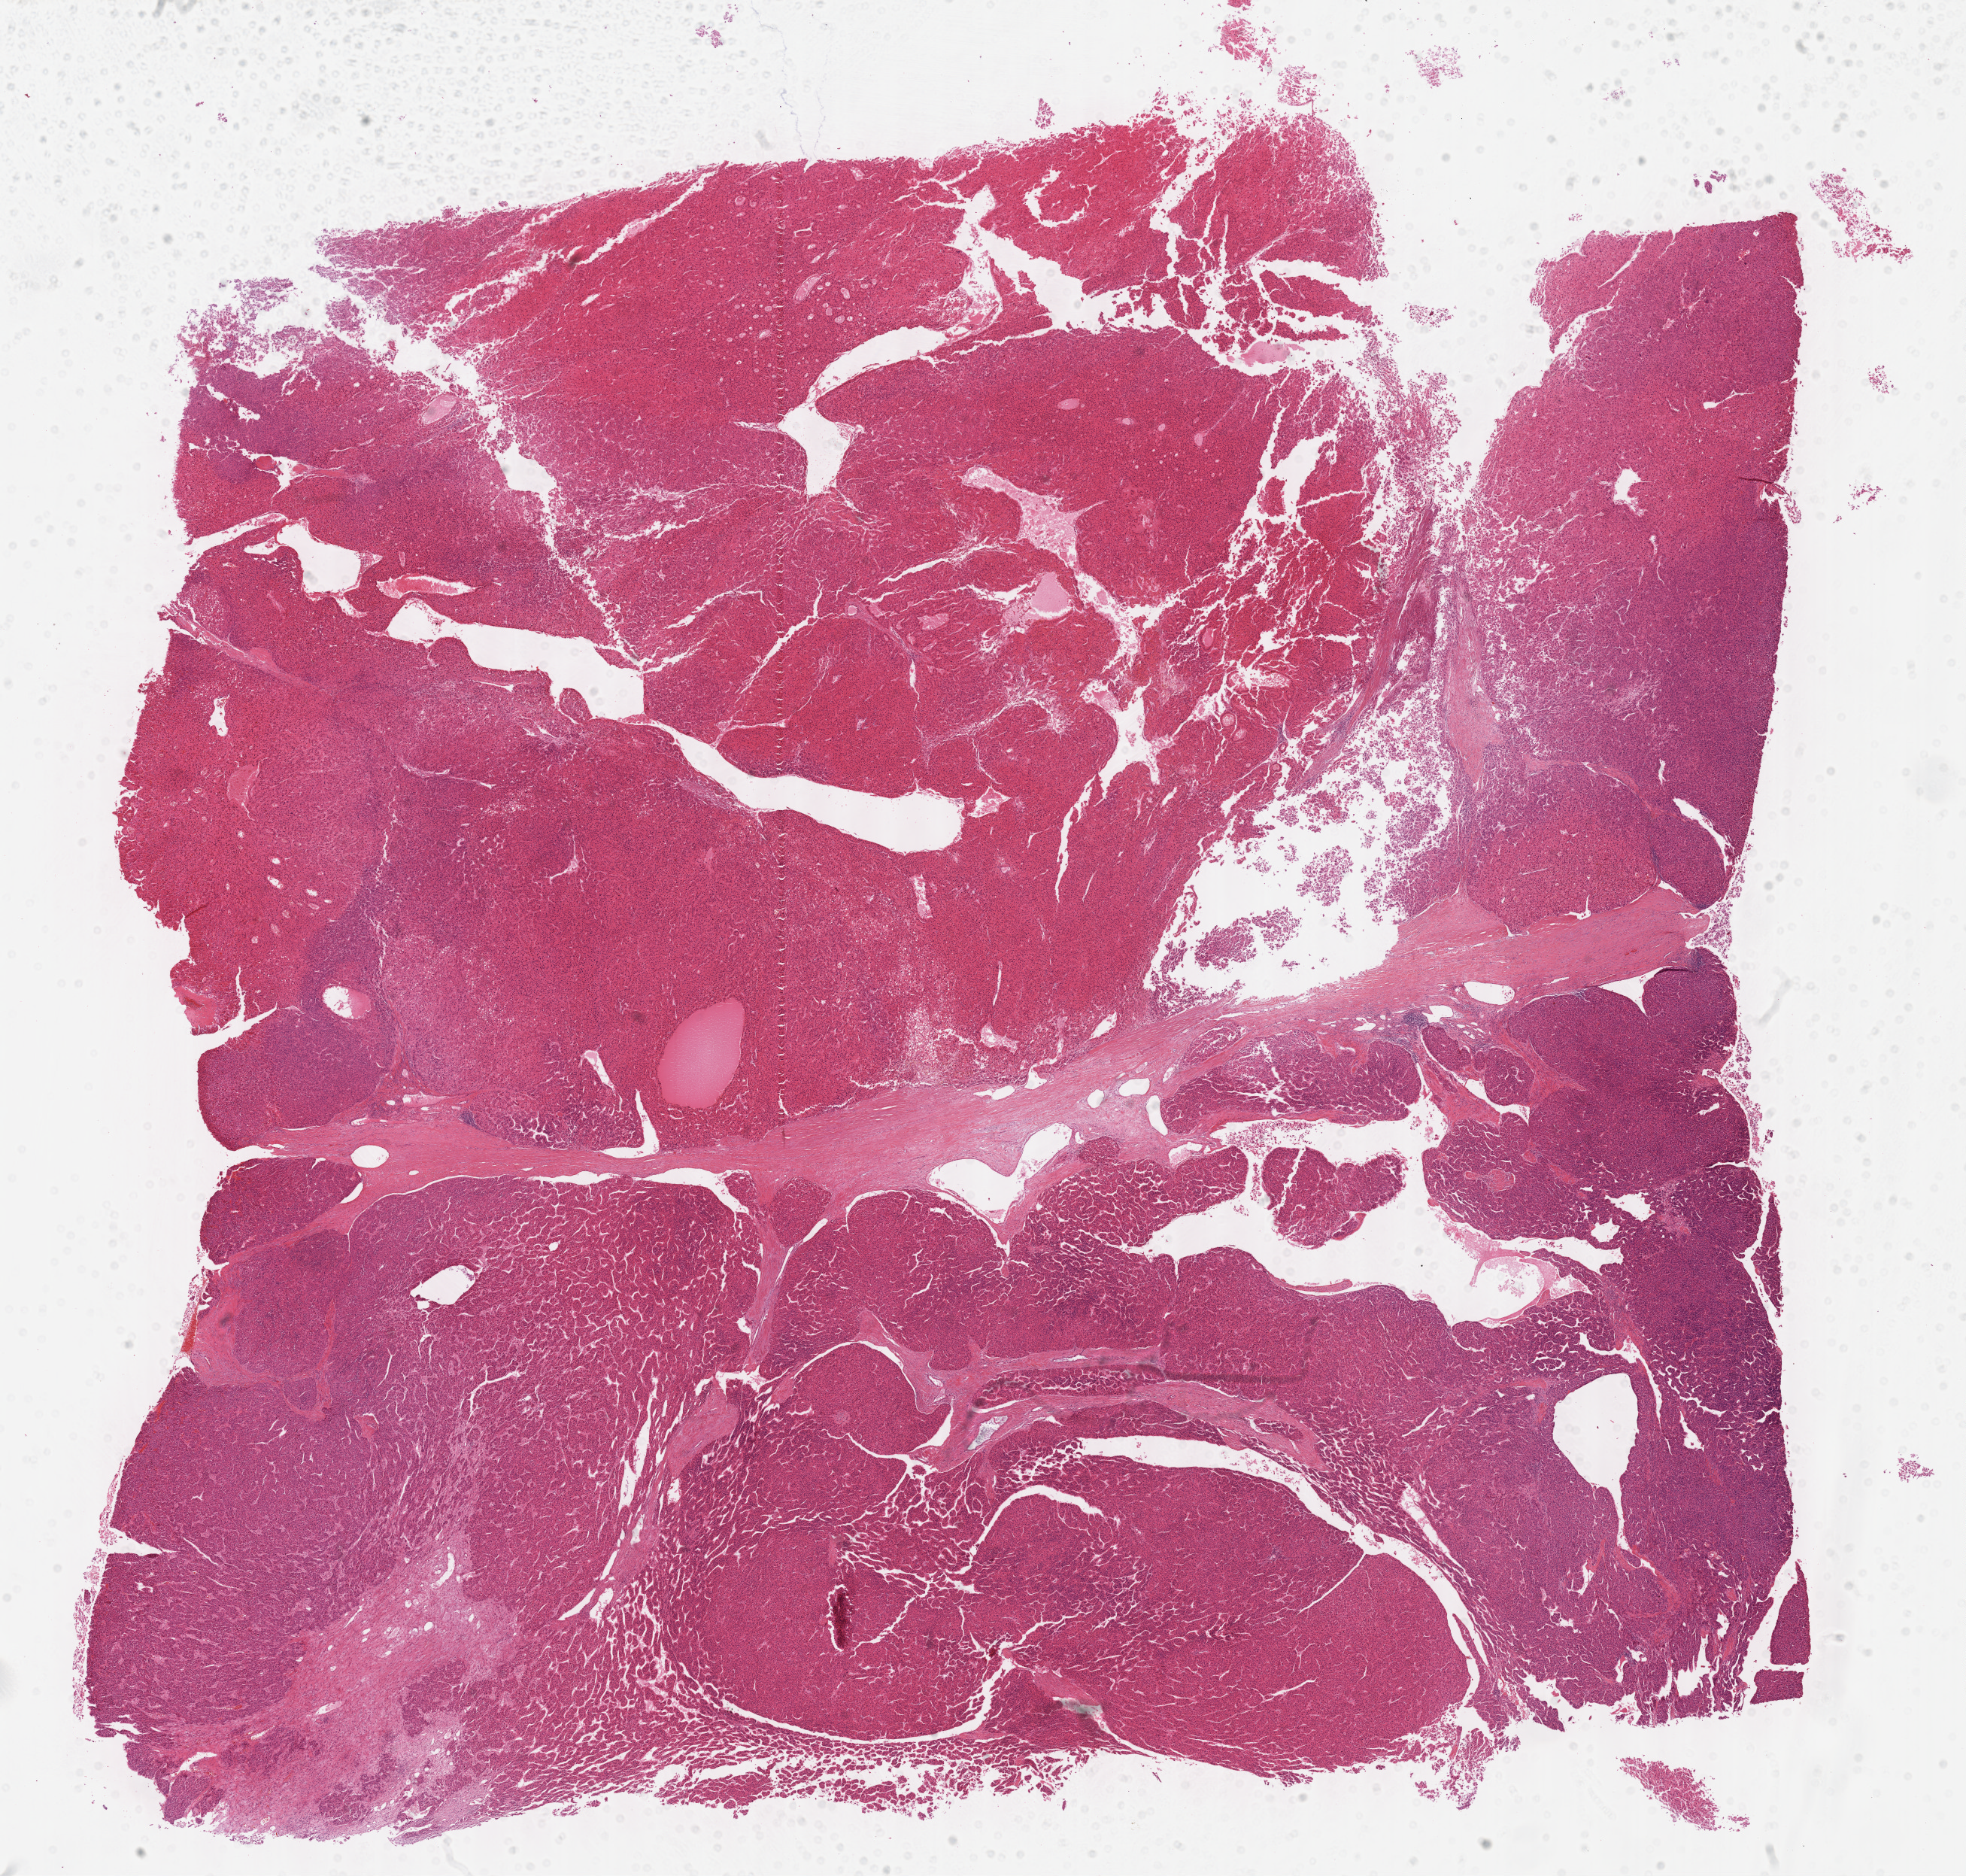
Whole-slide histology image, Hematoxylin and eosin (H&E) stained — low-resolution overview of the scanned area, about 21.1 x 20.2 mm (slide scanned at 40x); formalin-fixed paraffin-embedded (FFPE) diagnostic section; liver, primary tumour sample. Patient: male, age at initial diagnosis 72 years. Histologic grade: G3 (poorly differentiated).
AJCC pathologic stage: I (6th edition). Pathologic diagnosis: Hepatocellular carcinoma, NOS.